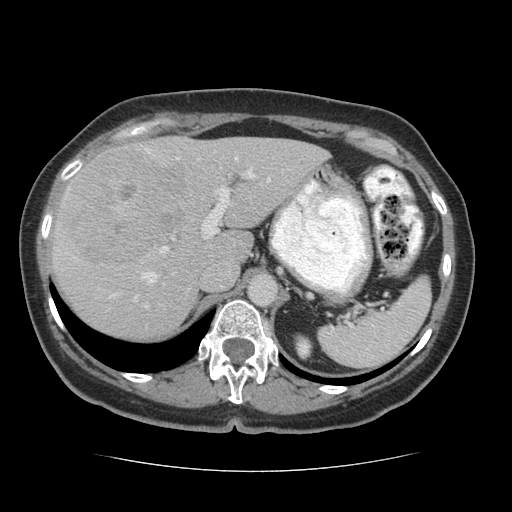
Contrast-enhanced abdominal CT (liver protocol), one axial slice; slice 44 of 75 in the series (ordered by position); reconstruction kernel STANDARD; 140 kVp; soft-tissue window (W 400 / L 40 HU); 2.5 mm slice thickness; 512 × 512 image matrix, field of view 360 × 360 mm. Case-level facts recorded for this patient, not image findings: diagnosis: hepatocellular carcinoma (patient treated with transarterial chemoembolisation; whether this scan precedes or follows treatment is not stated here); TNM stage (as recorded): Stage-I; Child-Pugh class: A; tumour differentiation: moderately differentiated; tumour nodularity: uninodular.
Structures marked on this image (semi-automatically segmented with operator editing):
- liver parenchyma outside the tumour (the mass and vessels are separate outlines, so this box may not span the whole liver): bounding box <52,136,328,338> (left, top, right, bottom; pixels)
- mass: <58,148,191,265>
- liver vessels: <66,149,271,301>